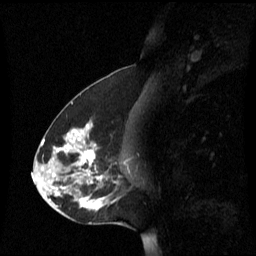
Breast MRI (dynamic contrast-enhanced), one sagittal slice; slice 29 of 60 in the series (ordered by position); dynamic contrast-enhanced series, image 2 of 3 at this slice position (ordered by acquisition); 1.5 T; TE 4.2 ms, TR 8.4 ms; 256 × 256 image matrix. Female patient, age 45 years. From the clinical record (not read from this slice): setting: breast cancer imaged before/during neoadjuvant chemotherapy; receptor status: HR-positive, HER2-negative.
Structures marked on this image (semi-automatic segmentation, software-assisted and operator-edited):
- analysis volume of interest (the breast-tissue region the enhancement analysis was run in; not a lesion): box from (x=38, y=122) to (x=131, y=221) px
- tumour enhancement mask (voxels above the 70 % enhancement threshold inside the analysis volume of interest): (x=56, y=124)–(x=107, y=211)